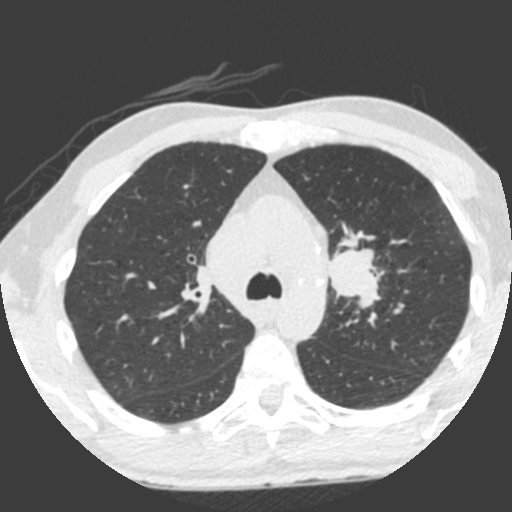
Axial slice from a low-dose chest CT screening exam. Third annual screen. Lung window (W 1500 / L -600 HU). 120 kVp. Slice 151 of 212 in the series. 512 × 512 image matrix, field of view 315 × 315 mm. Male, age 55 years at enrolment. Current smoker at enrolment.
• Expert reader's lesion annotation, bounding box (x1, y1, x2, y2) in pixels: (308, 232, 389, 323).
• Reader record for this screening exam (exam-level; its link to the box is not recorded): non-calcified nodule or mass ≥4 mm, left upper lobe, 49 × 29 mm, spiculated (stellate) margins, soft tissue attenuation, pre-existing on the prior screen: yes; interval growth: yes.
• Lung cancer was diagnosed 0 days after this screen: small cell carcinoma, NOS, left upper lobe, undifferentiated (G4), stage IV (AJCC 6th edition), 60 mm at pathology.